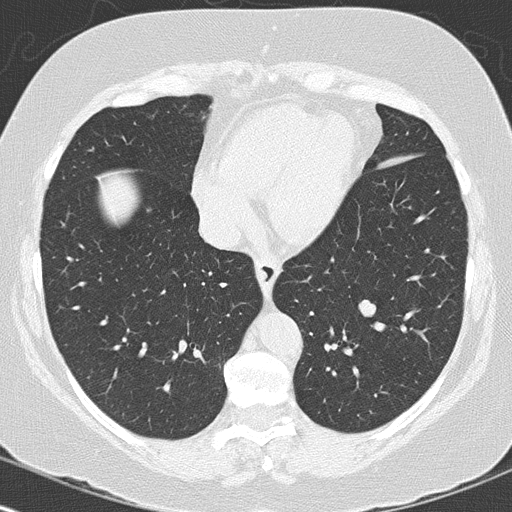
Chest CT (low-dose screening protocol), one axial image, baseline screening round, lung window (W 1500 / L -600 HU), 512 × 512 image matrix, field of view 316 × 316 mm. Female, age 60 years at enrolment. Former smoker at enrolment.
Lesion marked by an expert reader, bounding box <348,291,389,328> (left, top, right, bottom; pixels). Reader record for this screening exam (exam-level; its link to the box is not recorded): non-calcified nodule or mass ≥4 mm, left lower lobe, 12 × 10 mm, smooth margins, soft tissue attenuation. Official screen result: positive, change unspecified: nodule(s) >= 4 mm or enlarging nodule(s), mass(es), or other non-specific abnormalities suspicious for lung cancer. Participant outcome: lung cancer diagnosed 109 days after this screen — carcinoid tumor, NOS, left lower lobe, carcinoid, stage not assessed, 13 mm at pathology.